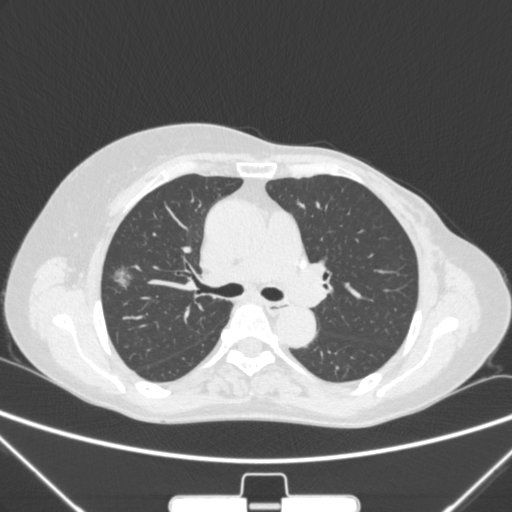
Chest CT, one axial slice; position 160 of 265 along the scan axis; 120 kVp; lung window (W 1500 / L -600 HU); 1 mm slice thickness; 512 × 512 image matrix, field of view 350 × 350 mm. Female patient, age 64 years. Case-level facts recorded for this patient, not image findings: clinical TNM (as recorded): T1c N0 M0; histopathological grade: G1-2.
Structures marked on this image (bounding box drawn by a radiologist):
- lung tumour (recorded histology: adenocarcinoma): bounding box [x1, y1, x2, y2] px = [100, 262, 139, 303]